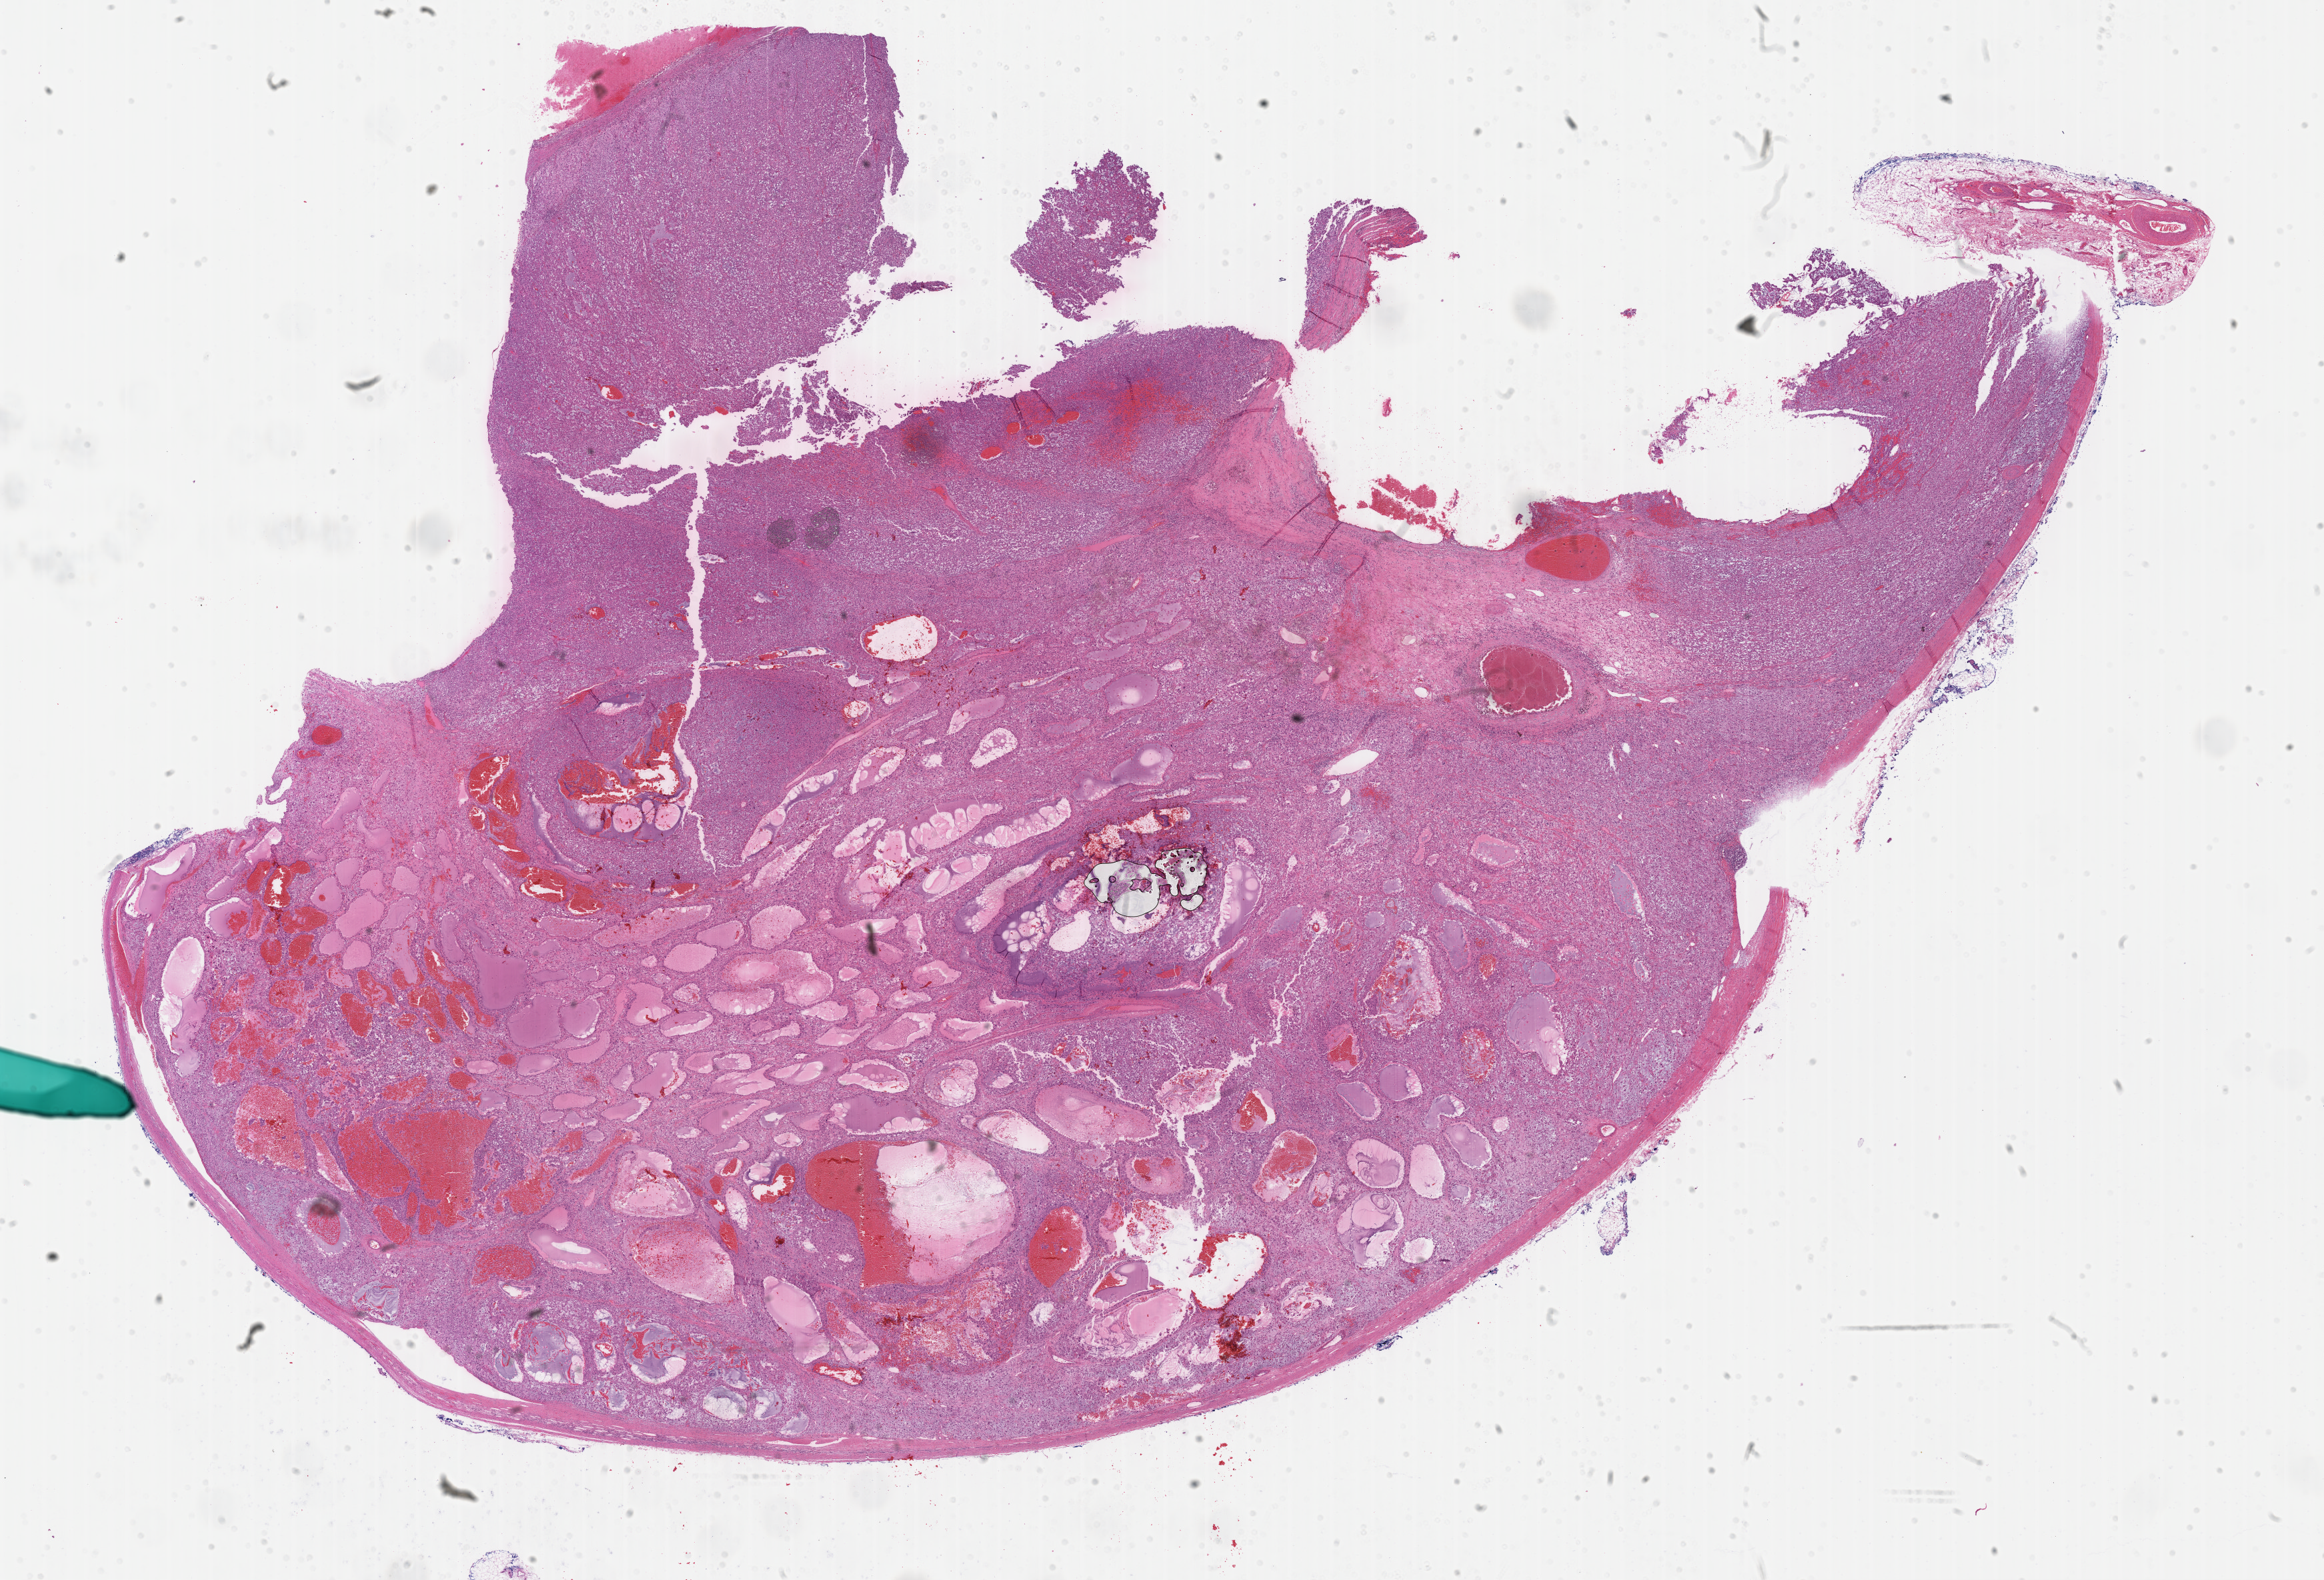
Digitized Hematoxylin and eosin (H&E) stained tissue section (whole slide), low-resolution overview of the scanned area, about 28.2 x 19.2 mm (from a 40x scan), formalin-fixed paraffin-embedded (FFPE) diagnostic section, adrenal cortex, primary tumour sample. Female patient; age at initial diagnosis 26 years.
- laterality: right
- diagnosis: Adrenal cortical carcinoma (cortex of adrenal gland)